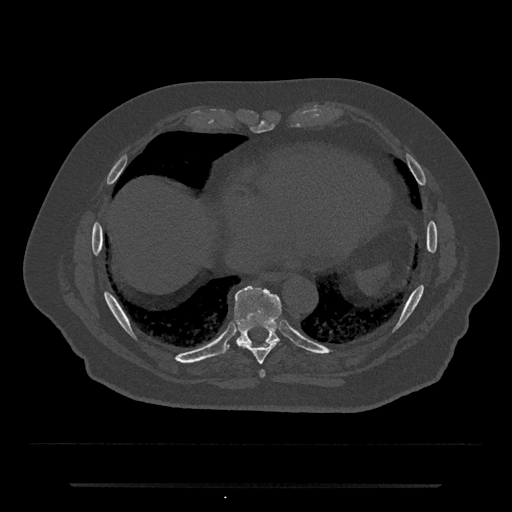
CT including the spine, one axial slice; slice 782 of 797 in the series (ordered by position); reconstruction kernel Br40s/3; 120 kVp; bone window (W 1800 / L 400 HU); 512 × 512 image matrix, field of view 434 × 434 mm. Male patient, age 80 years. From the clinical record (not read from this slice): primary cancer: prostate; vertebrae with lytic lesions (as recorded): L1, T11.
Outlined on this slice (semi-automatically segmented with operator editing):
- T8 vertebra: bounding box <239,342,278,364> (left, top, right, bottom; pixels)
- T9 vertebra: <219,286,281,355>